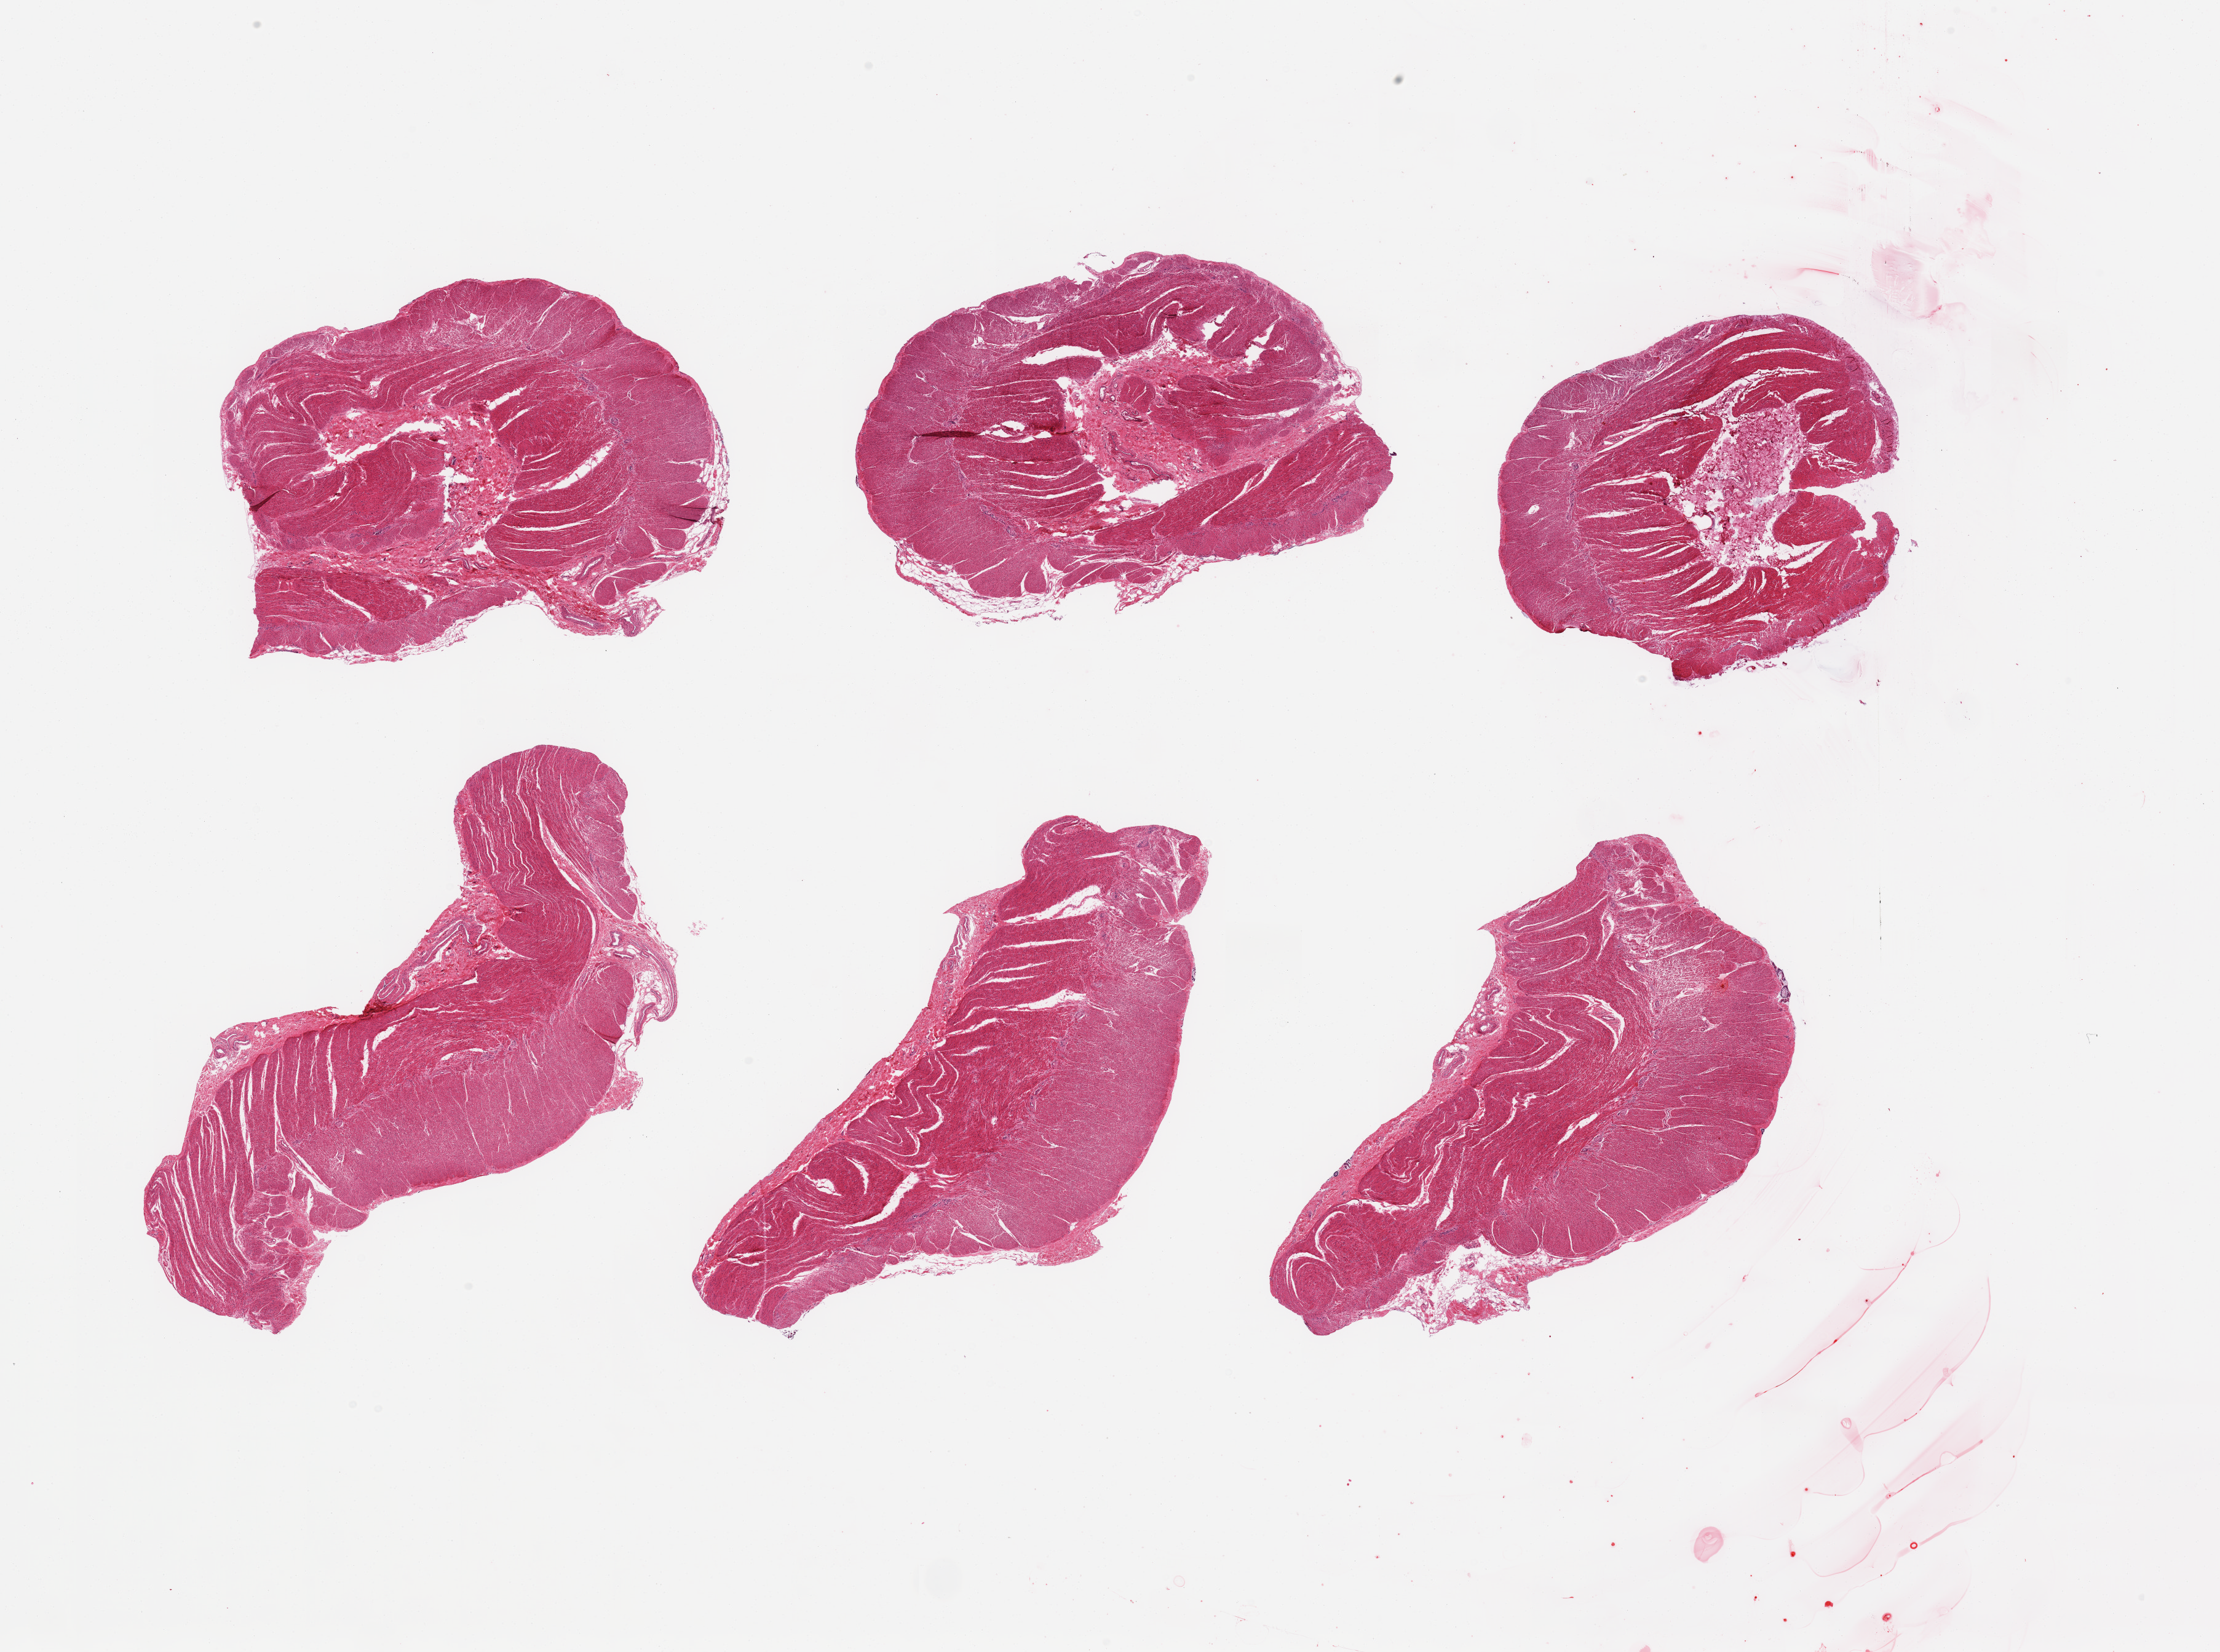
Haematoxylin and eosin whole-slide image, low-resolution overview of the scanned area, about 28.5 x 21.2 mm (slide scanned at 20x); PAXgene-fixed, paraffin-embedded tissue; sampled site (target tissue): sigmoid colon; donor tissue sample.
• reviewer comment on this tissue sample: 6 pieces; target muscularis